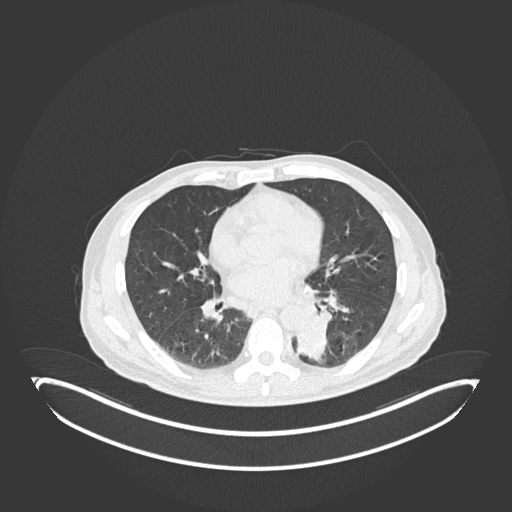
Chest CT, one axial slice. Position 86 of 251 along the scan axis. 120 kVp. Lung window (W 1500 / L -600 HU). 1 mm slice thickness. 512 × 512 image matrix, field of view 500 × 500 mm. Patient: male, 72 years. Case-level facts recorded for this patient, not image findings: clinical TNM (as recorded): T2b N0 M1.
Outlined on this slice (rectangle marked by the reading radiologist):
- lung tumour (recorded histology: adenocarcinoma): box from (x=289, y=310) to (x=334, y=363) px